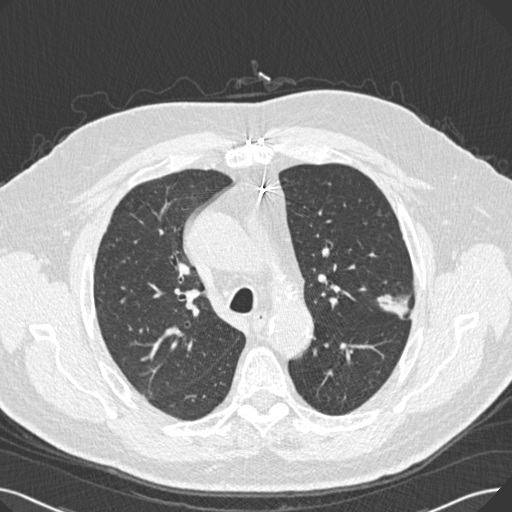
Low-dose screening chest CT, one axial slice; slice 181 of 269 in the series (ordered by position); reconstruction kernel B30f; 120 kVp; lung window (W 1500 / L -600 HU); 1 mm slice thickness; 512 × 512 image matrix, field of view 370 × 370 mm.
Outlined on this slice (expert manual segmentation):
- lesion 1 (tumor, upper lobe of left lung): bounding box <377,294,411,319> (left, top, right, bottom; pixels)